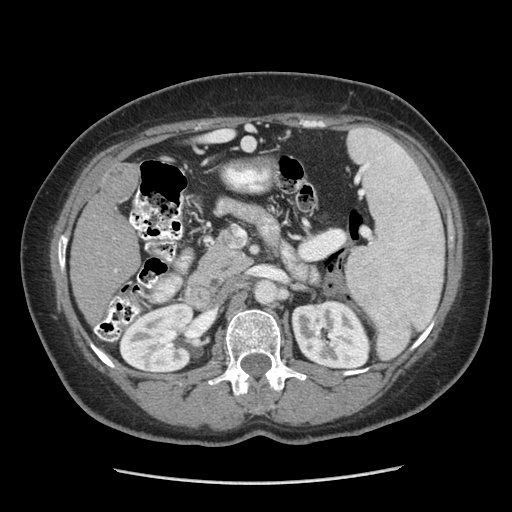
Contrast-enhanced abdominal CT (liver protocol), one axial slice; position 134 of 185 along the scan axis; 140 kVp; soft-tissue window (W 400 / L 40 HU); 2.5 mm slice thickness; 512 × 512 image matrix, field of view 360 × 360 mm. From the clinical record (not read from this slice): diagnosis: hepatocellular carcinoma (patient treated with transarterial chemoembolisation; whether this scan precedes or follows treatment is not stated here); TNM stage (as recorded): Stage-I; Child-Pugh class: A; tumour nodularity: uninodular.
Annotated regions visible in this slice (semi-automatic segmentation, software-assisted and operator-edited):
- liver parenchyma outside the tumour (the mass and vessels are separate outlines, so this box may not span the whole liver): bounding box (x1, y1, x2, y2) in pixels: (70, 164, 140, 320)
- mass: (99, 164, 137, 213)
- liver vessels: (115, 270, 117, 272)